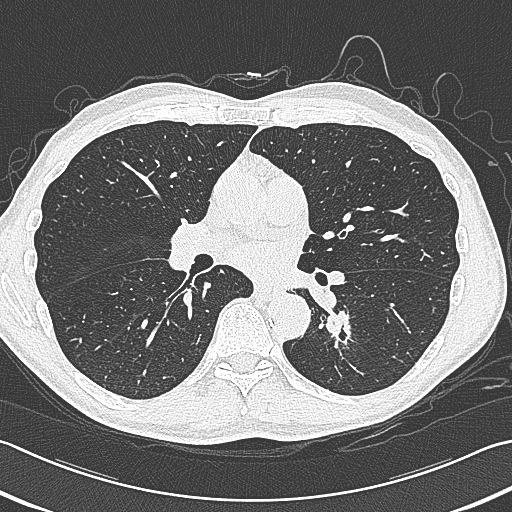
Low-dose screening chest CT, axial slice; baseline annual screen; lung window (W 1500 / L -600 HU). Male, age 59 years at enrolment. Former smoker at enrolment.
Lesion marked by an expert reader, box from (x=313, y=294) to (x=375, y=353) px. Reader record for this screening exam (exam-level; its link to the box is not recorded): non-calcified nodule or mass ≥4 mm, left lower lobe, 15 × 15 mm, smooth margins, soft tissue attenuation. Official screen result: positive, change unspecified: nodule(s) >= 4 mm or enlarging nodule(s), mass(es), or other non-specific abnormalities suspicious for lung cancer. Lung cancer was diagnosed 17 days after this screen: squamous cell carcinoma, large cell, nonkeratinizing, NOS, left lower lobe, poorly differentiated (G3), stage IB (AJCC 6th edition), 31 mm at pathology.